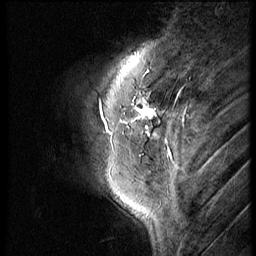
Breast MRI (dynamic contrast-enhanced), one sagittal slice; position 15 of 56 along the scan axis; 3 images stored at this slice position (order not interpretable as contrast timing); 1.5 T; TE 4.2 ms, TR 9 ms; 2.5 mm slice thickness; 256 × 256 image matrix. Patient: female, 46 years. From the clinical record (not read from this slice): setting: breast cancer imaged before/during neoadjuvant chemotherapy; receptor status: HER2-positive.
Annotated regions visible in this slice (semi-automatic segmentation, software-assisted and operator-edited):
- analysis volume of interest (the breast-tissue region the enhancement analysis was run in; not a lesion): bounding box [x1, y1, x2, y2] px = [77, 86, 164, 161]
- tumour enhancement mask (voxels above the 140 % enhancement threshold inside the analysis volume of interest): [138, 102, 155, 118]